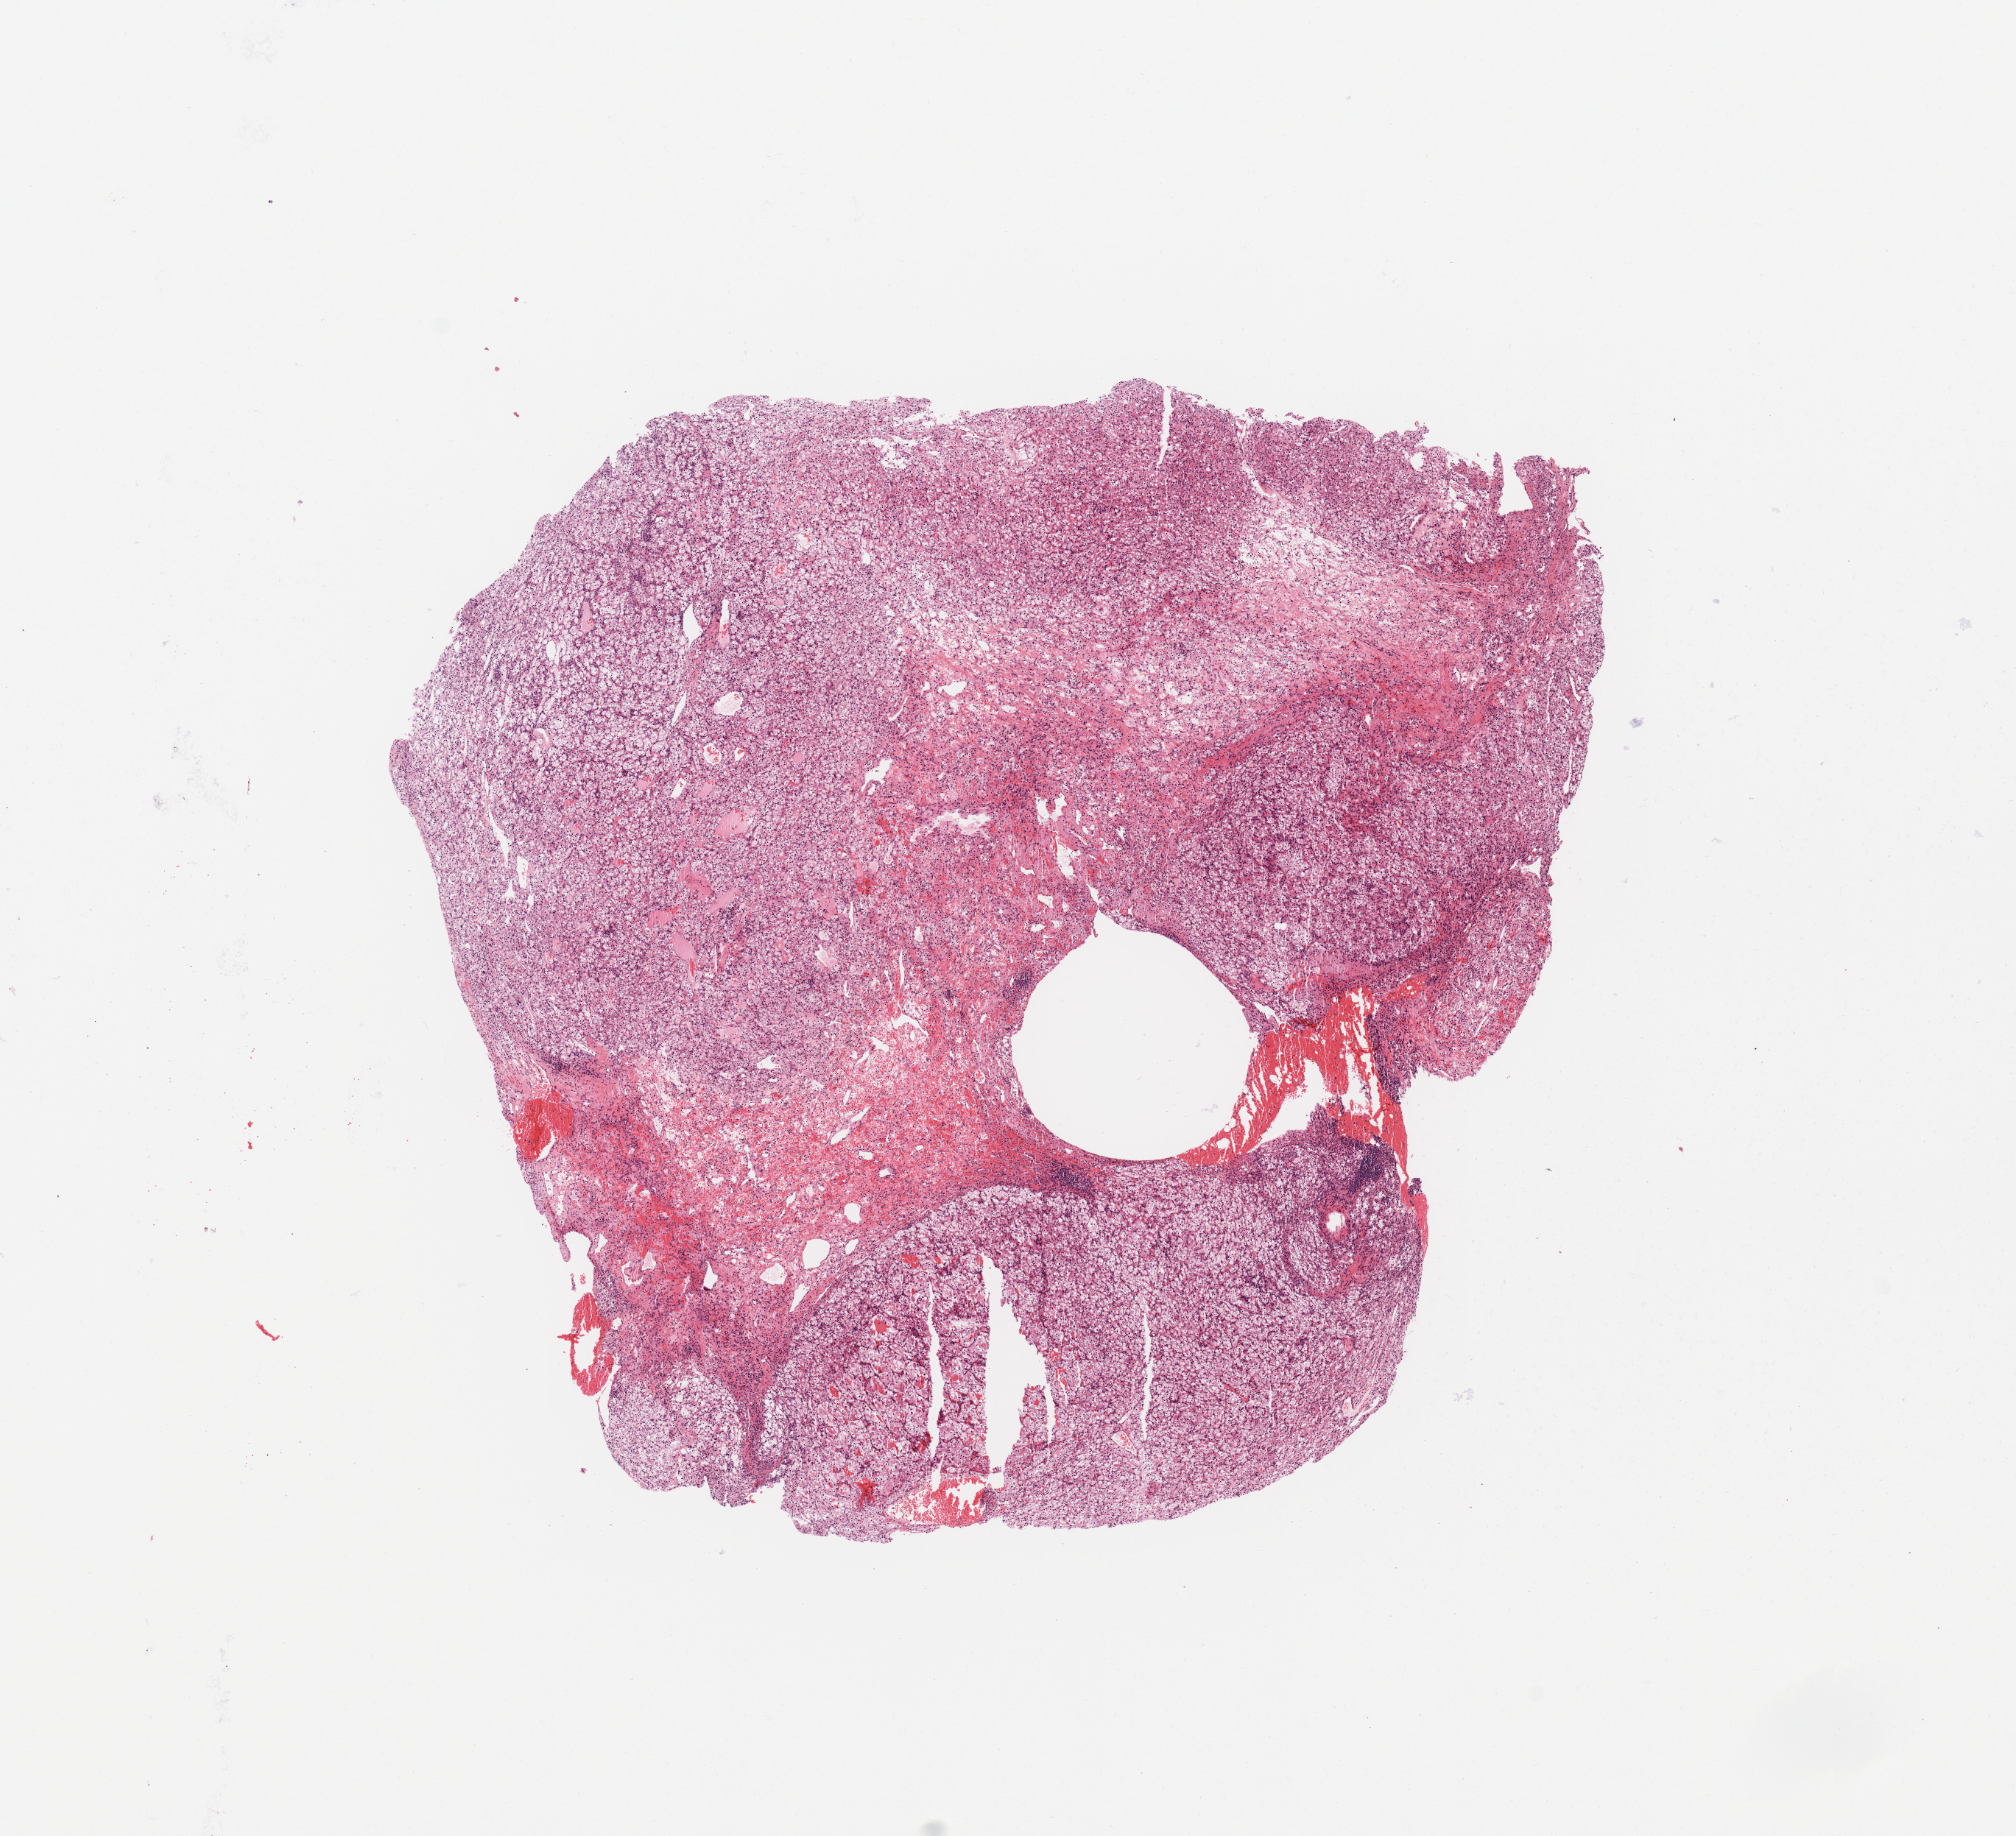
Whole-slide histology image, H&E-stained — low-resolution overview of the scanned area, about 10.8 x 9.9 mm (slide scanned at 20x). Tumour tissue sample, sampled site: kidney. Female, 66 y/o. Pathologist review of this section (percent, as recorded): tumour nuclei 85%, necrosis 5%.
Diagnosis: Renal cell carcinoma, NOS.